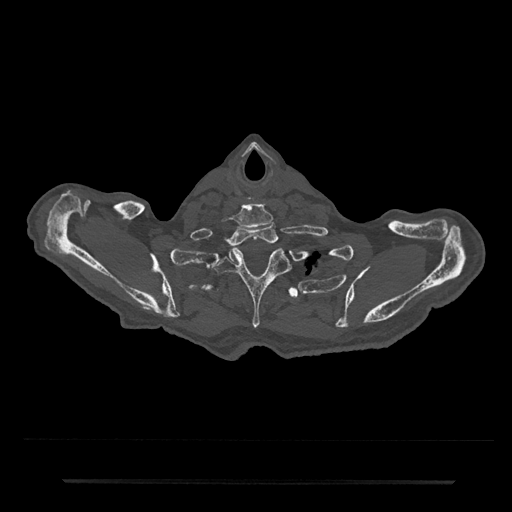
CT including the spine, one axial slice; reconstruction kernel Br40s/3; bone window (W 1800 / L 400 HU); 0.5 mm slice thickness; 512 × 512 image matrix, field of view 427 × 427 mm. Male patient, age 74 years. Case-level facts recorded for this patient, not image findings: primary cancer: prostate.
Structures marked on this image (semi-automatically segmented with operator editing):
- T1 vertebra: box from (x=229, y=223) to (x=278, y=256) px
- T2 vertebra: (x=212, y=248)–(x=291, y=329)
- T3 vertebra: (x=216, y=287)–(x=299, y=300)